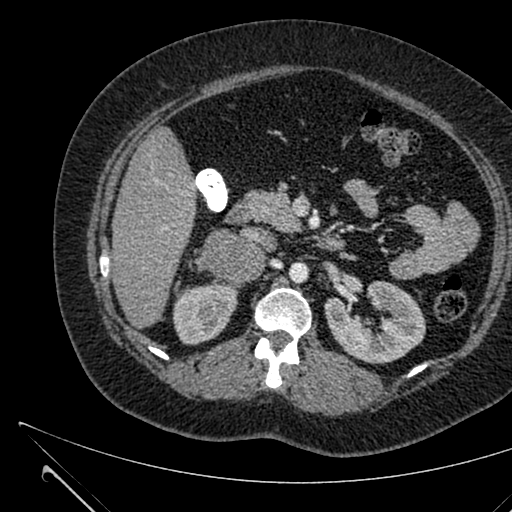
Contrast-enhanced abdominal CT, one axial slice. Position 364 of 731 along the scan axis. Soft-tissue window (W 400 / L 40 HU). 1 mm slice thickness. 512 × 512 image matrix. Female patient, age 36 years. Case-level facts recorded for this patient, not image findings: diagnosis: adrenocortical carcinoma; tumour side: right adrenal; tumour size at pathology: 10 cm; Ki-67 index: 20 %; stage (as recorded): 4.
Annotated regions visible in this slice (semi-automatically segmented with operator editing):
- mass: box from (x=200, y=228) to (x=265, y=284) px